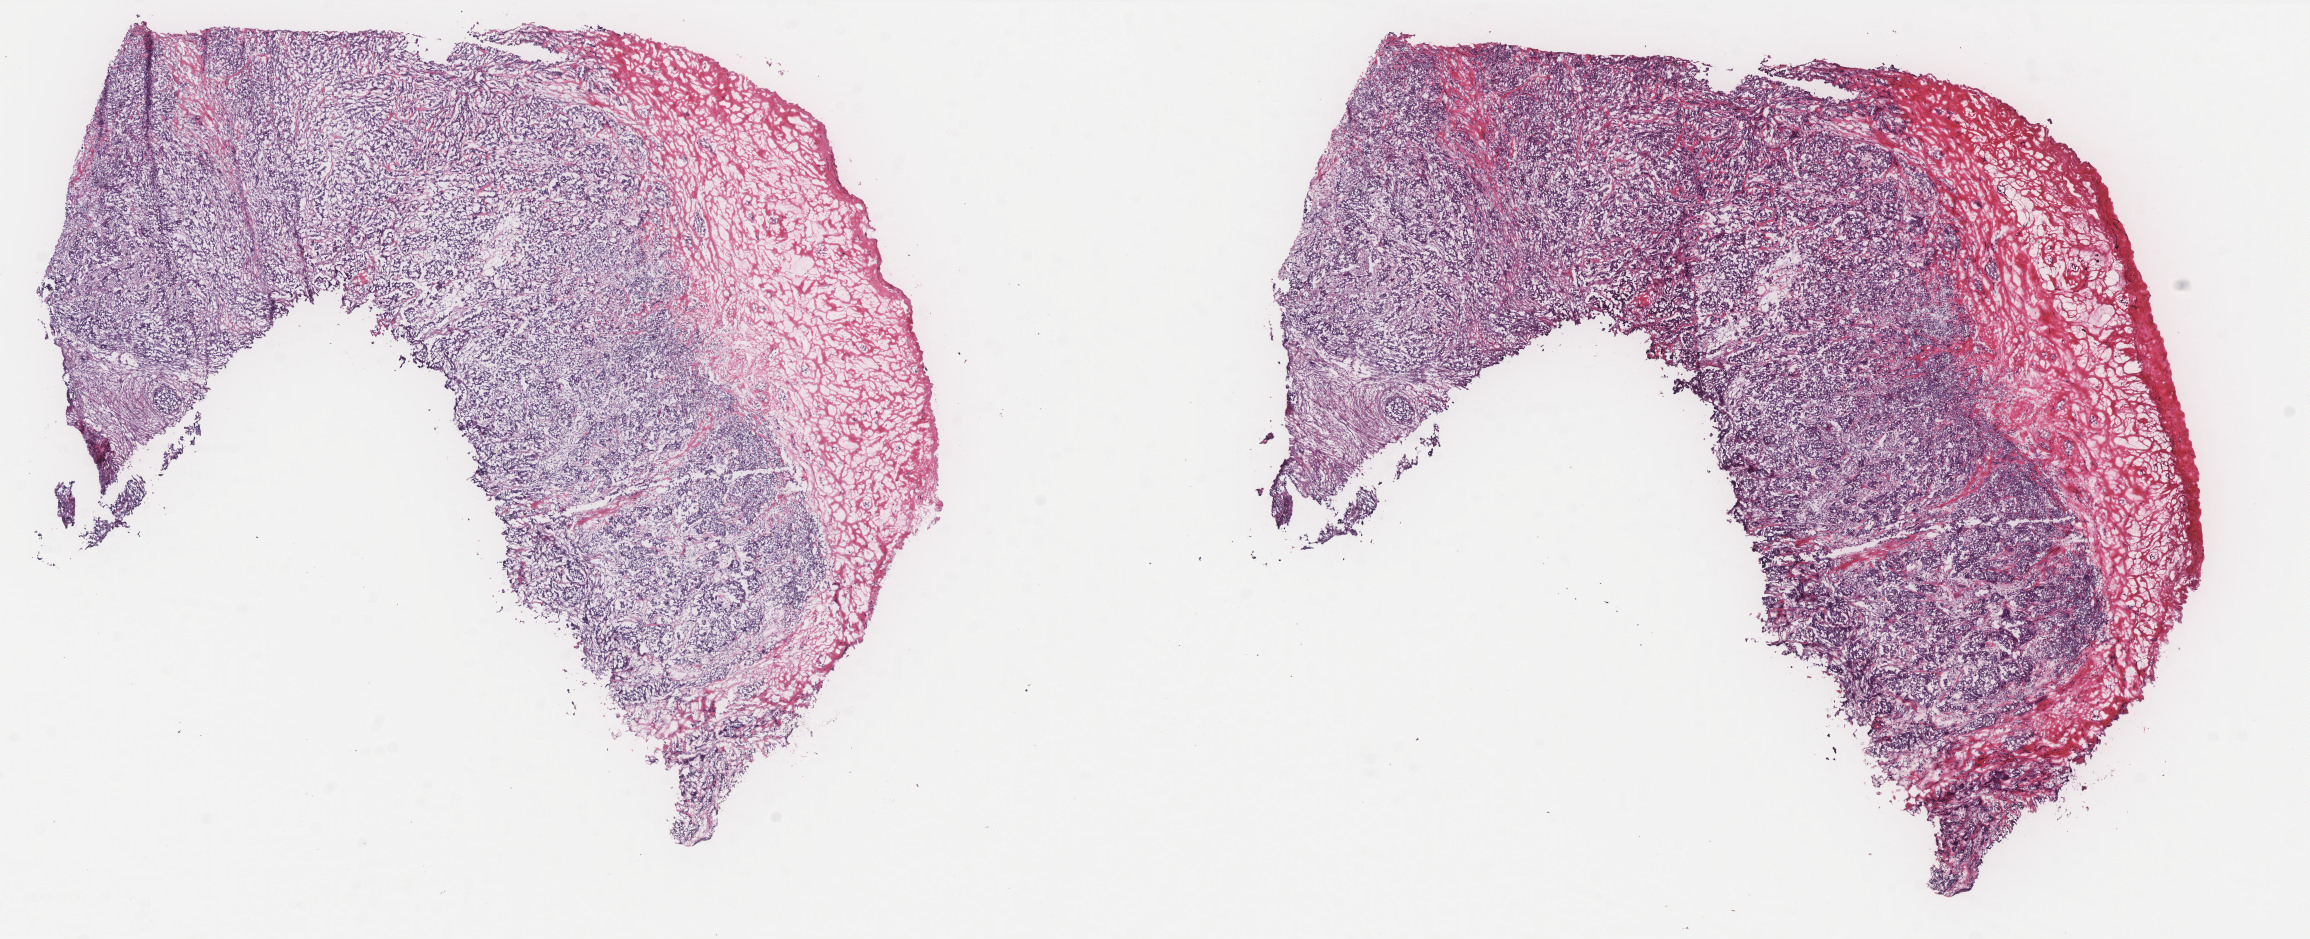
H&E-stained whole-slide image — whole scanned area (about 18.5 x 7.5 mm, from a 40x scan) shown as a low-resolution overview, frozen section, primary tumour sample from the breast. Female patient; age at initial diagnosis 36 years. Slide review estimates, as recorded: tumour cells 85%, tumour nuclei 85%, normal cells 0%, stromal cells 15%, necrosis 0%. Inflammatory infiltration, as recorded: lymphocyte infiltration 2%, monocyte infiltration 0%, neutrophil infiltration 0%.
Pathologic diagnosis: Infiltrating duct carcinoma, NOS. Laterality: left. AJCC pathologic stage: IIIA.